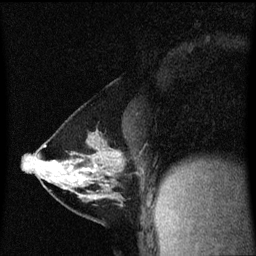
Breast MRI (dynamic contrast-enhanced), one sagittal slice; position 30 of 60 along the scan axis; dynamic contrast-enhanced series, image 2 of 3 at this slice position (ordered by acquisition); 1.5 T; TE 4.2 ms, TR 8.4 ms; 2 mm slice thickness; 256 × 256 image matrix. Patient: female, 40 years. Case-level facts recorded for this patient, not image findings: setting: breast cancer imaged before/during neoadjuvant chemotherapy; receptor status: triple-negative.
Annotated regions visible in this slice (semi-automatically segmented with operator editing):
- analysis volume of interest (the breast-tissue region the enhancement analysis was run in; not a lesion): bounding box <34,142,126,199> (left, top, right, bottom; pixels)
- tumour enhancement mask (voxels above the 70 % enhancement threshold inside the analysis volume of interest): <84,166,96,171>